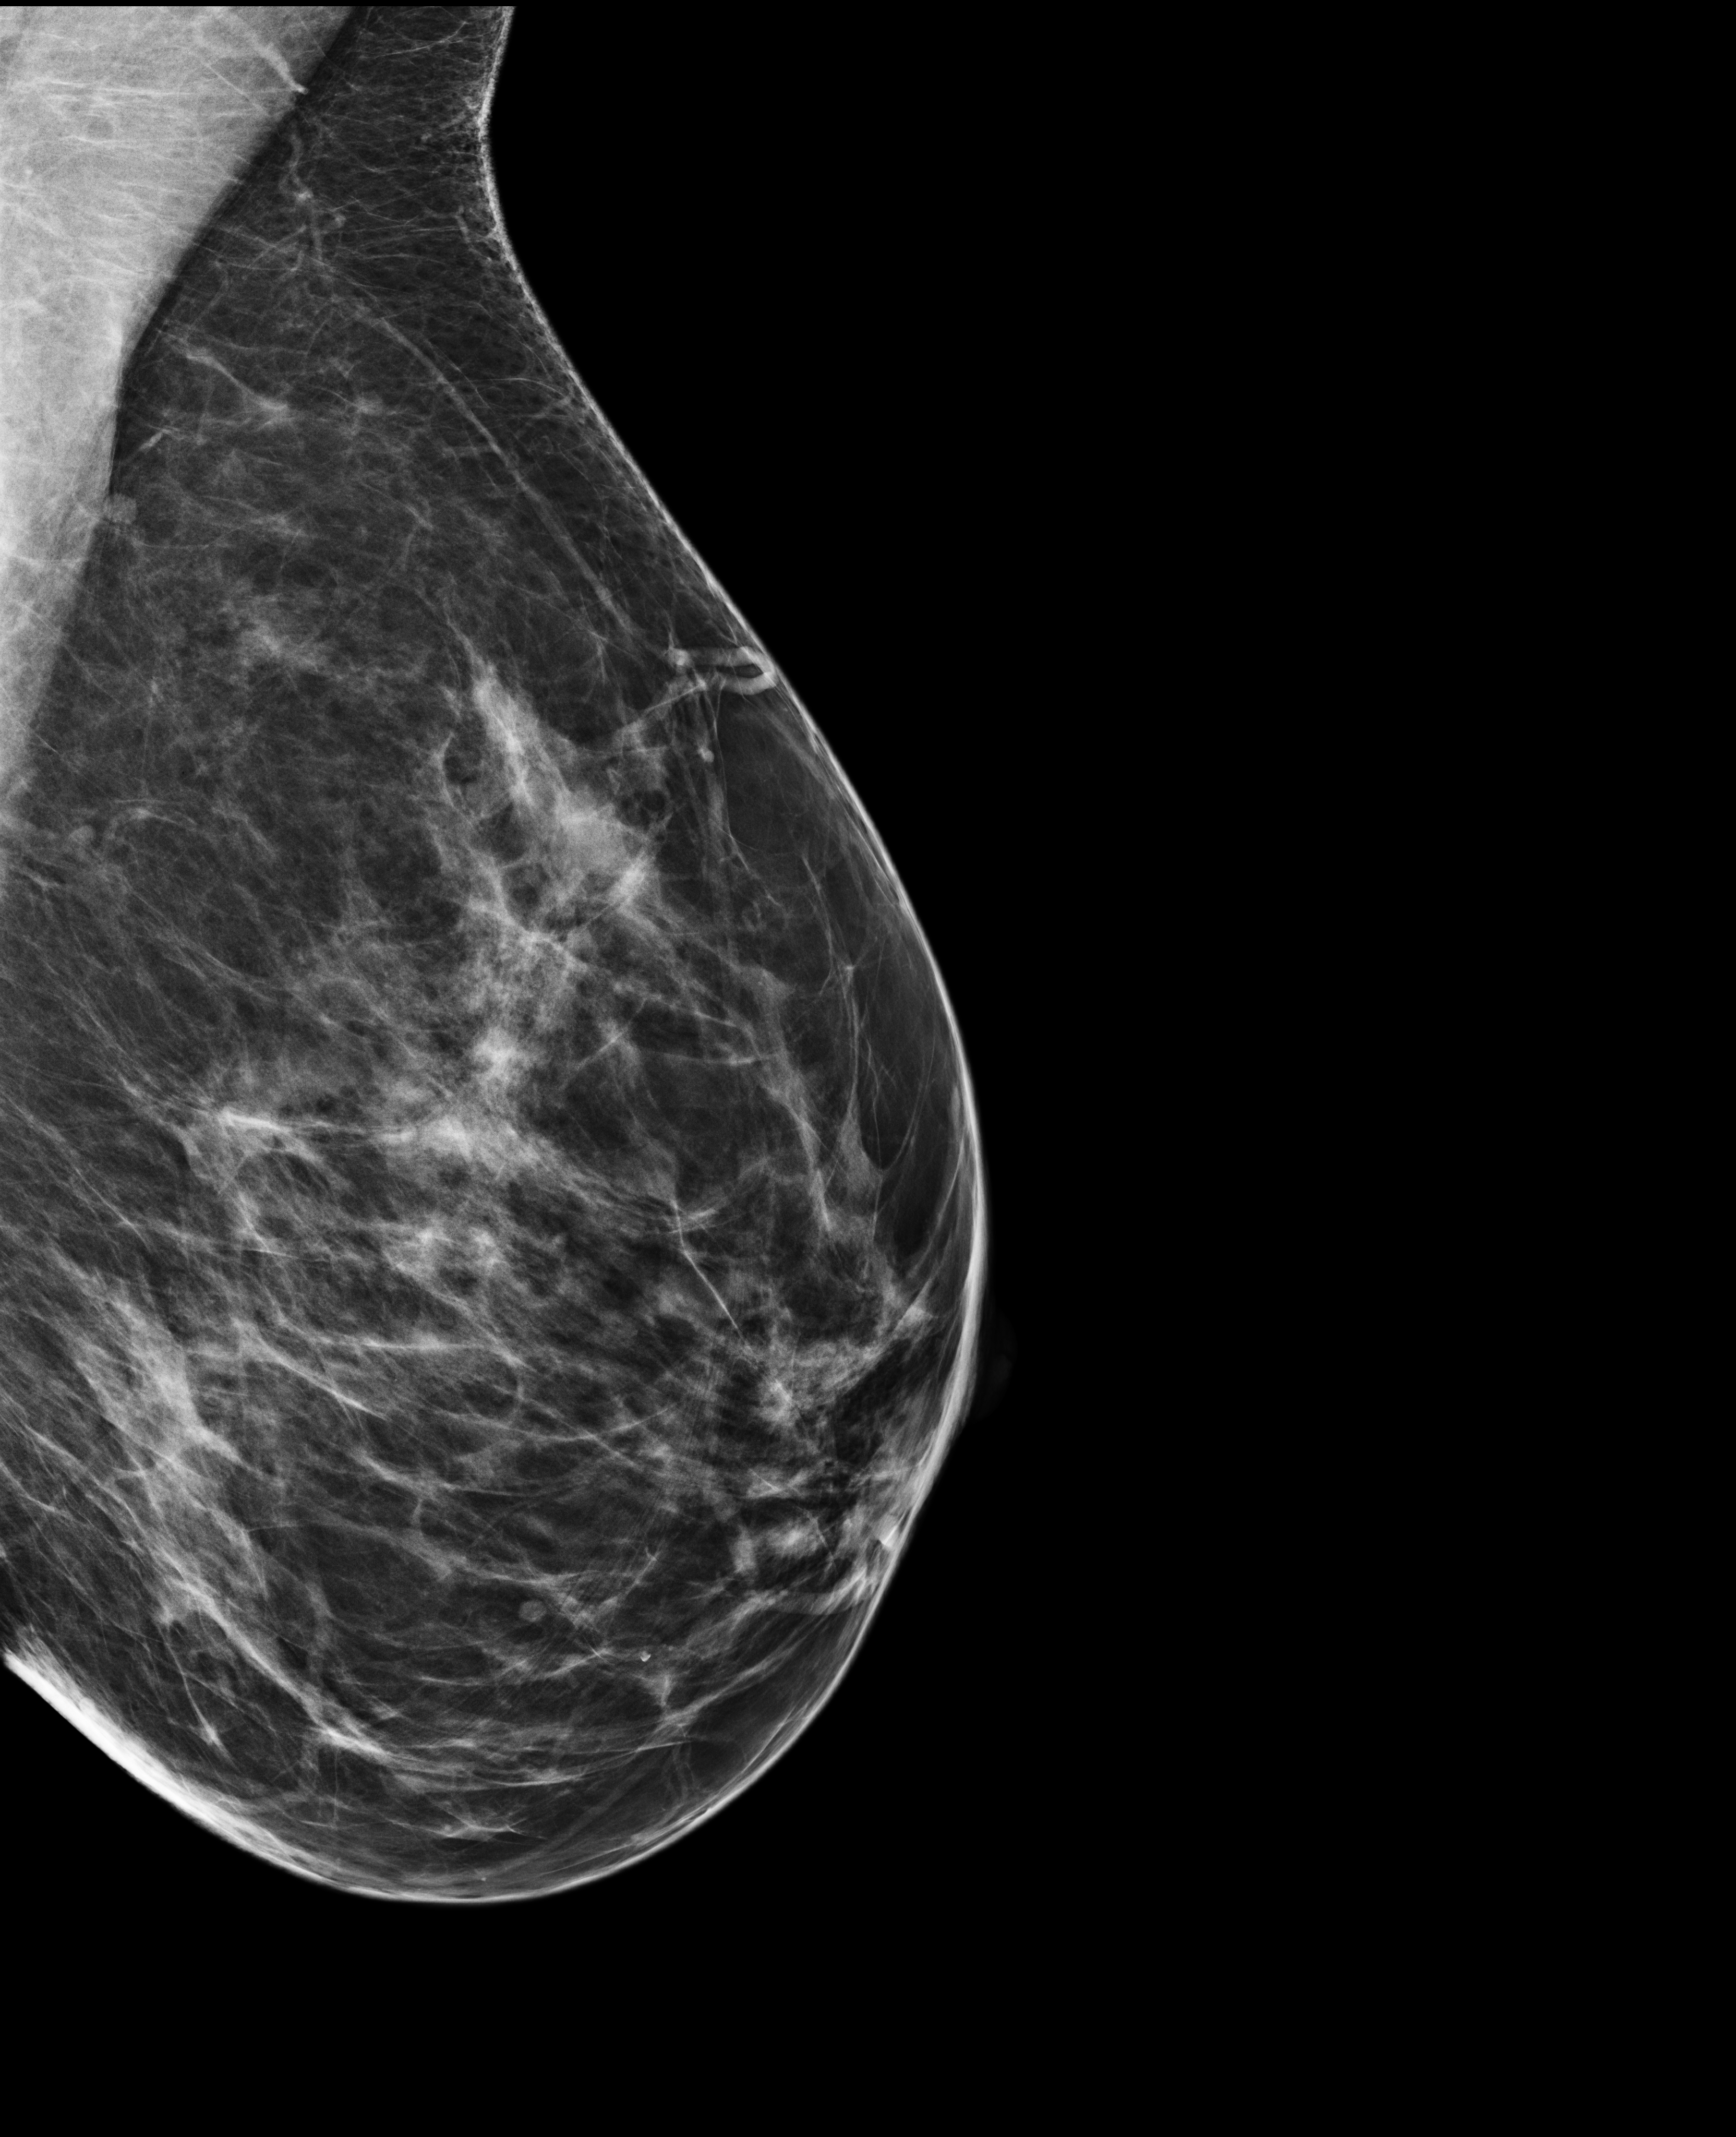
Screening examination. Patient aged 48 years (female).
Image type: full-field digital mammogram. Breast: left. Projection: medio-lateral oblique projection.